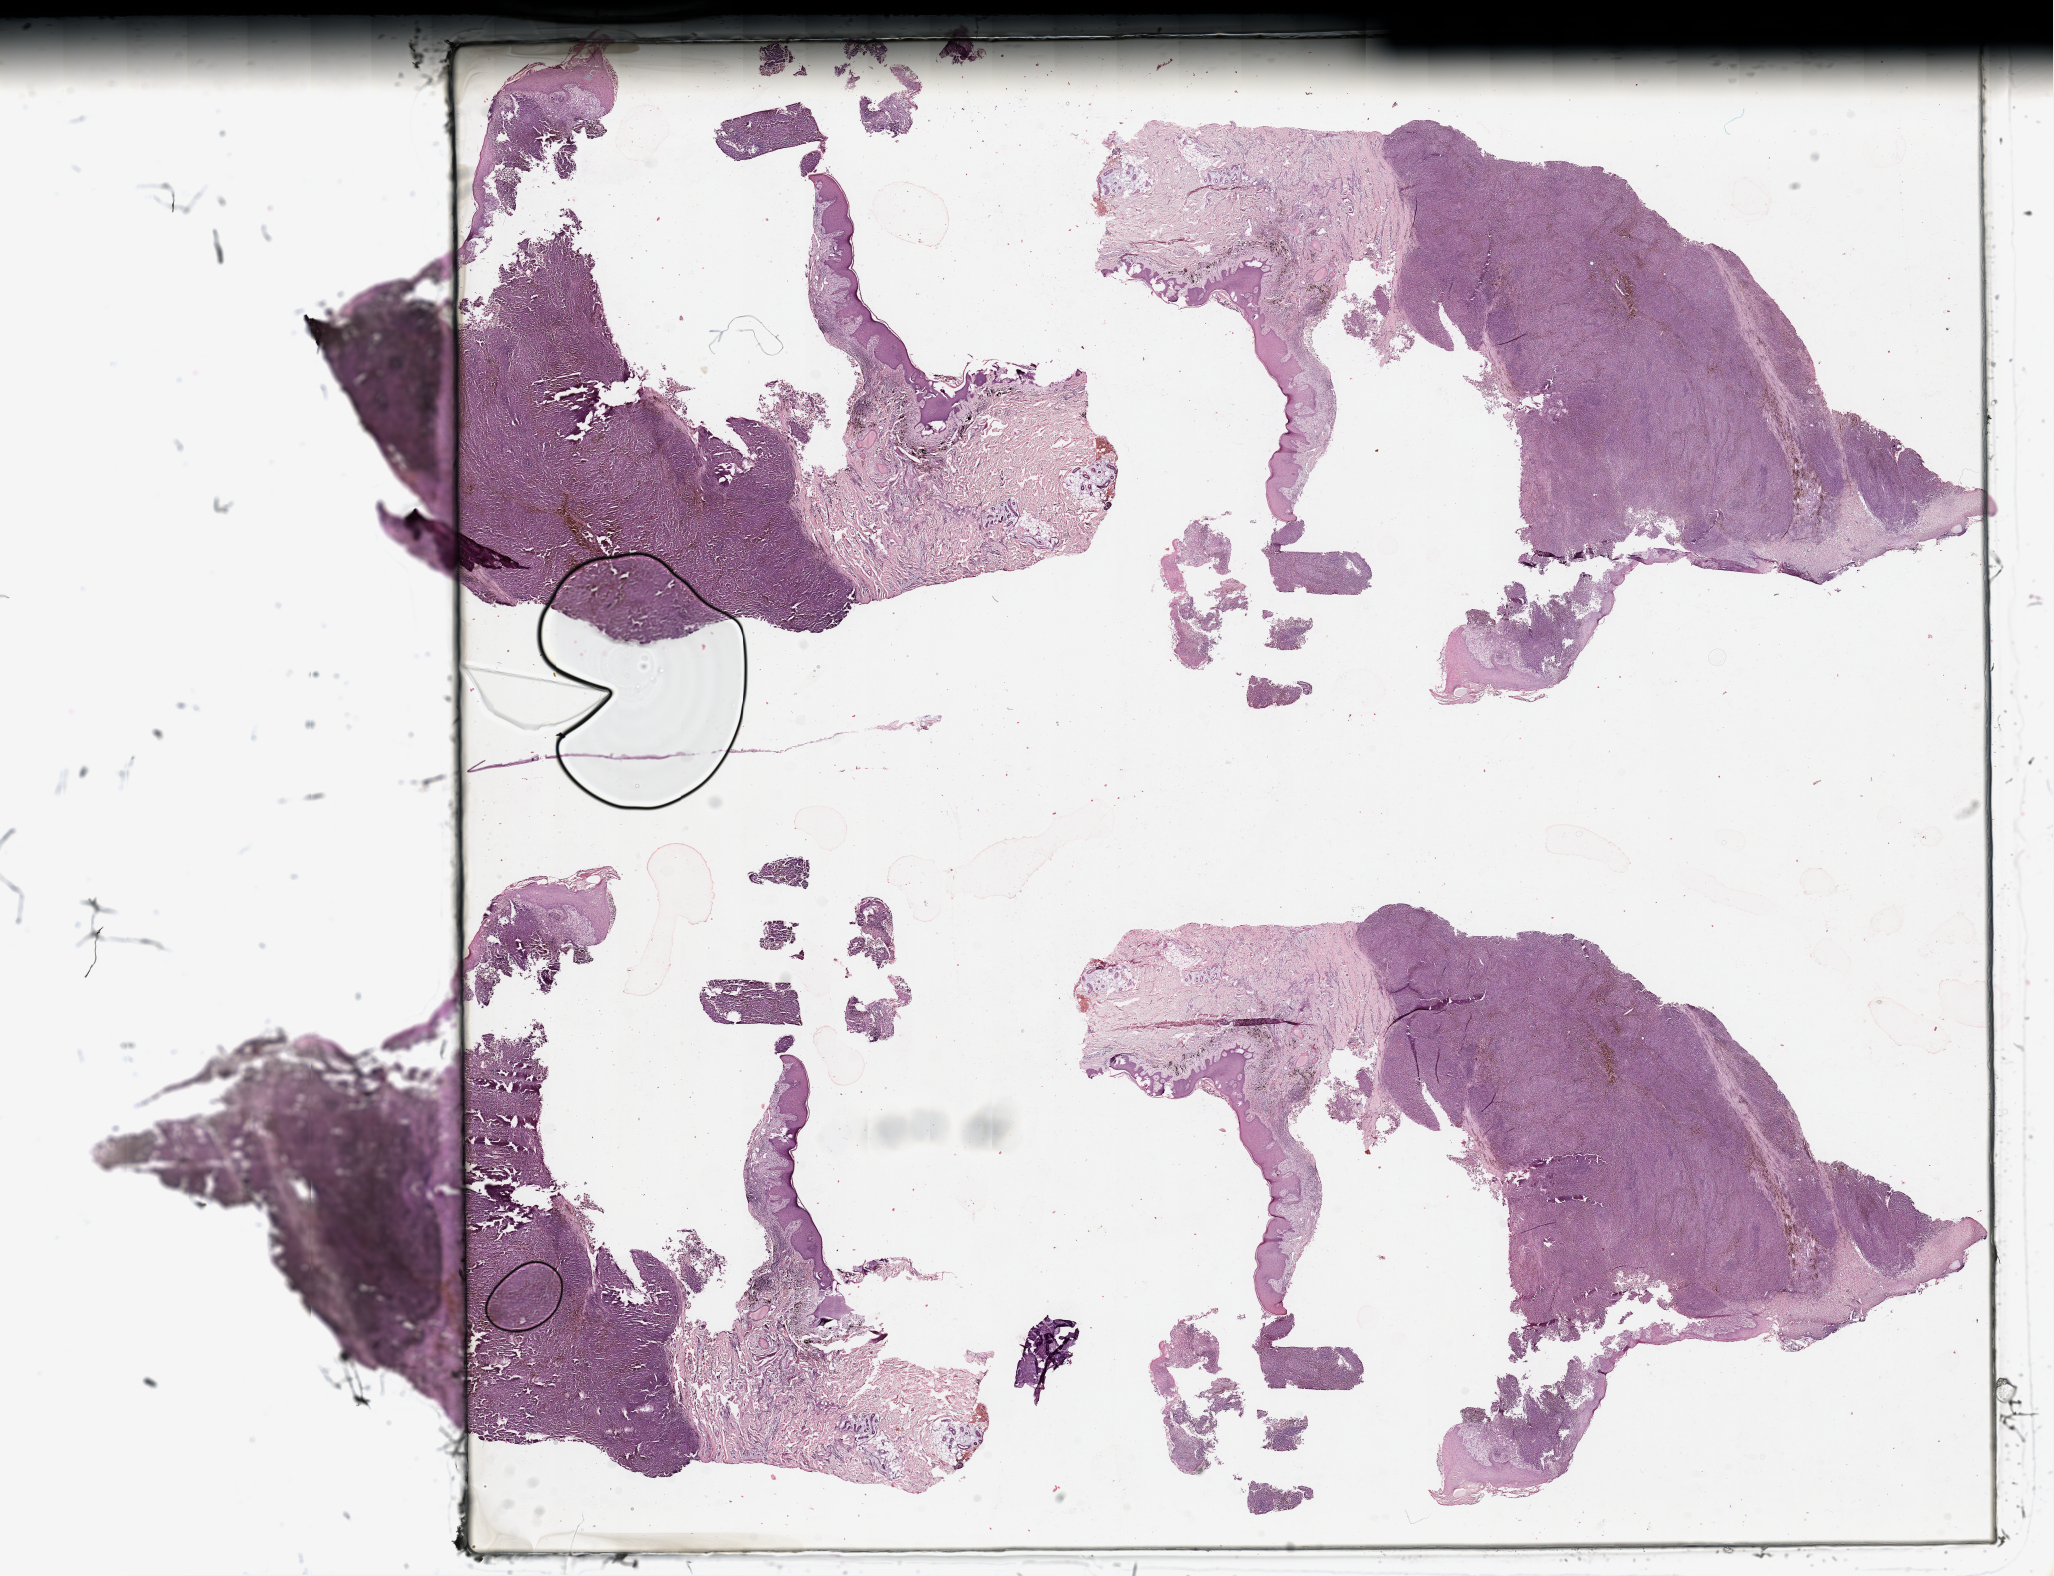
Whole-slide histology image, Hematoxylin and eosin (H&E) stained — whole scanned area (about 32.5 x 24.9 mm) shown as a low-resolution overview, tumour tissue sample, sampled site: trunk. Patient: male, age 60 years. Composition of this section per pathologist review: tumour nuclei 80%, necrosis 5%.
- primary tumour site (as recorded): trunk
- histologic diagnosis: Malignant melanoma, NOS